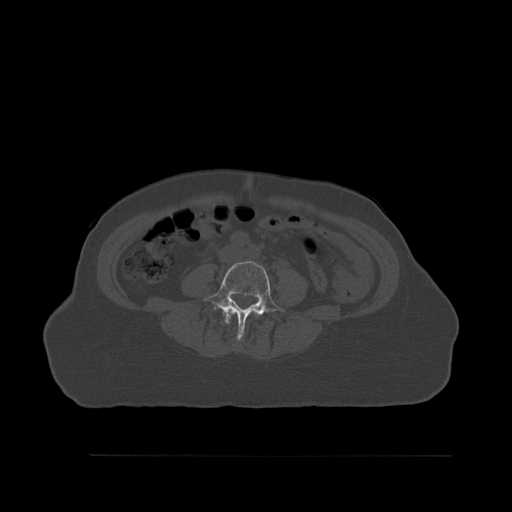
CT including the spine, one axial slice. Slice 208 of 527 in the series (ordered by position). Bone window (W 1800 / L 400 HU). 1.5 mm slice thickness. 512 × 512 image matrix, field of view 470 × 470 mm. Female patient, age 73 years. Case-level facts recorded for this patient, not image findings: primary cancer: breast; vertebrae with lytic lesions (as recorded): L2.
Outlined on this slice (semi-automatic segmentation, software-assisted and operator-edited):
- L3 vertebra: bounding box (x1, y1, x2, y2) in pixels: (225, 308, 259, 324)
- L4 vertebra: (203, 261, 284, 340)